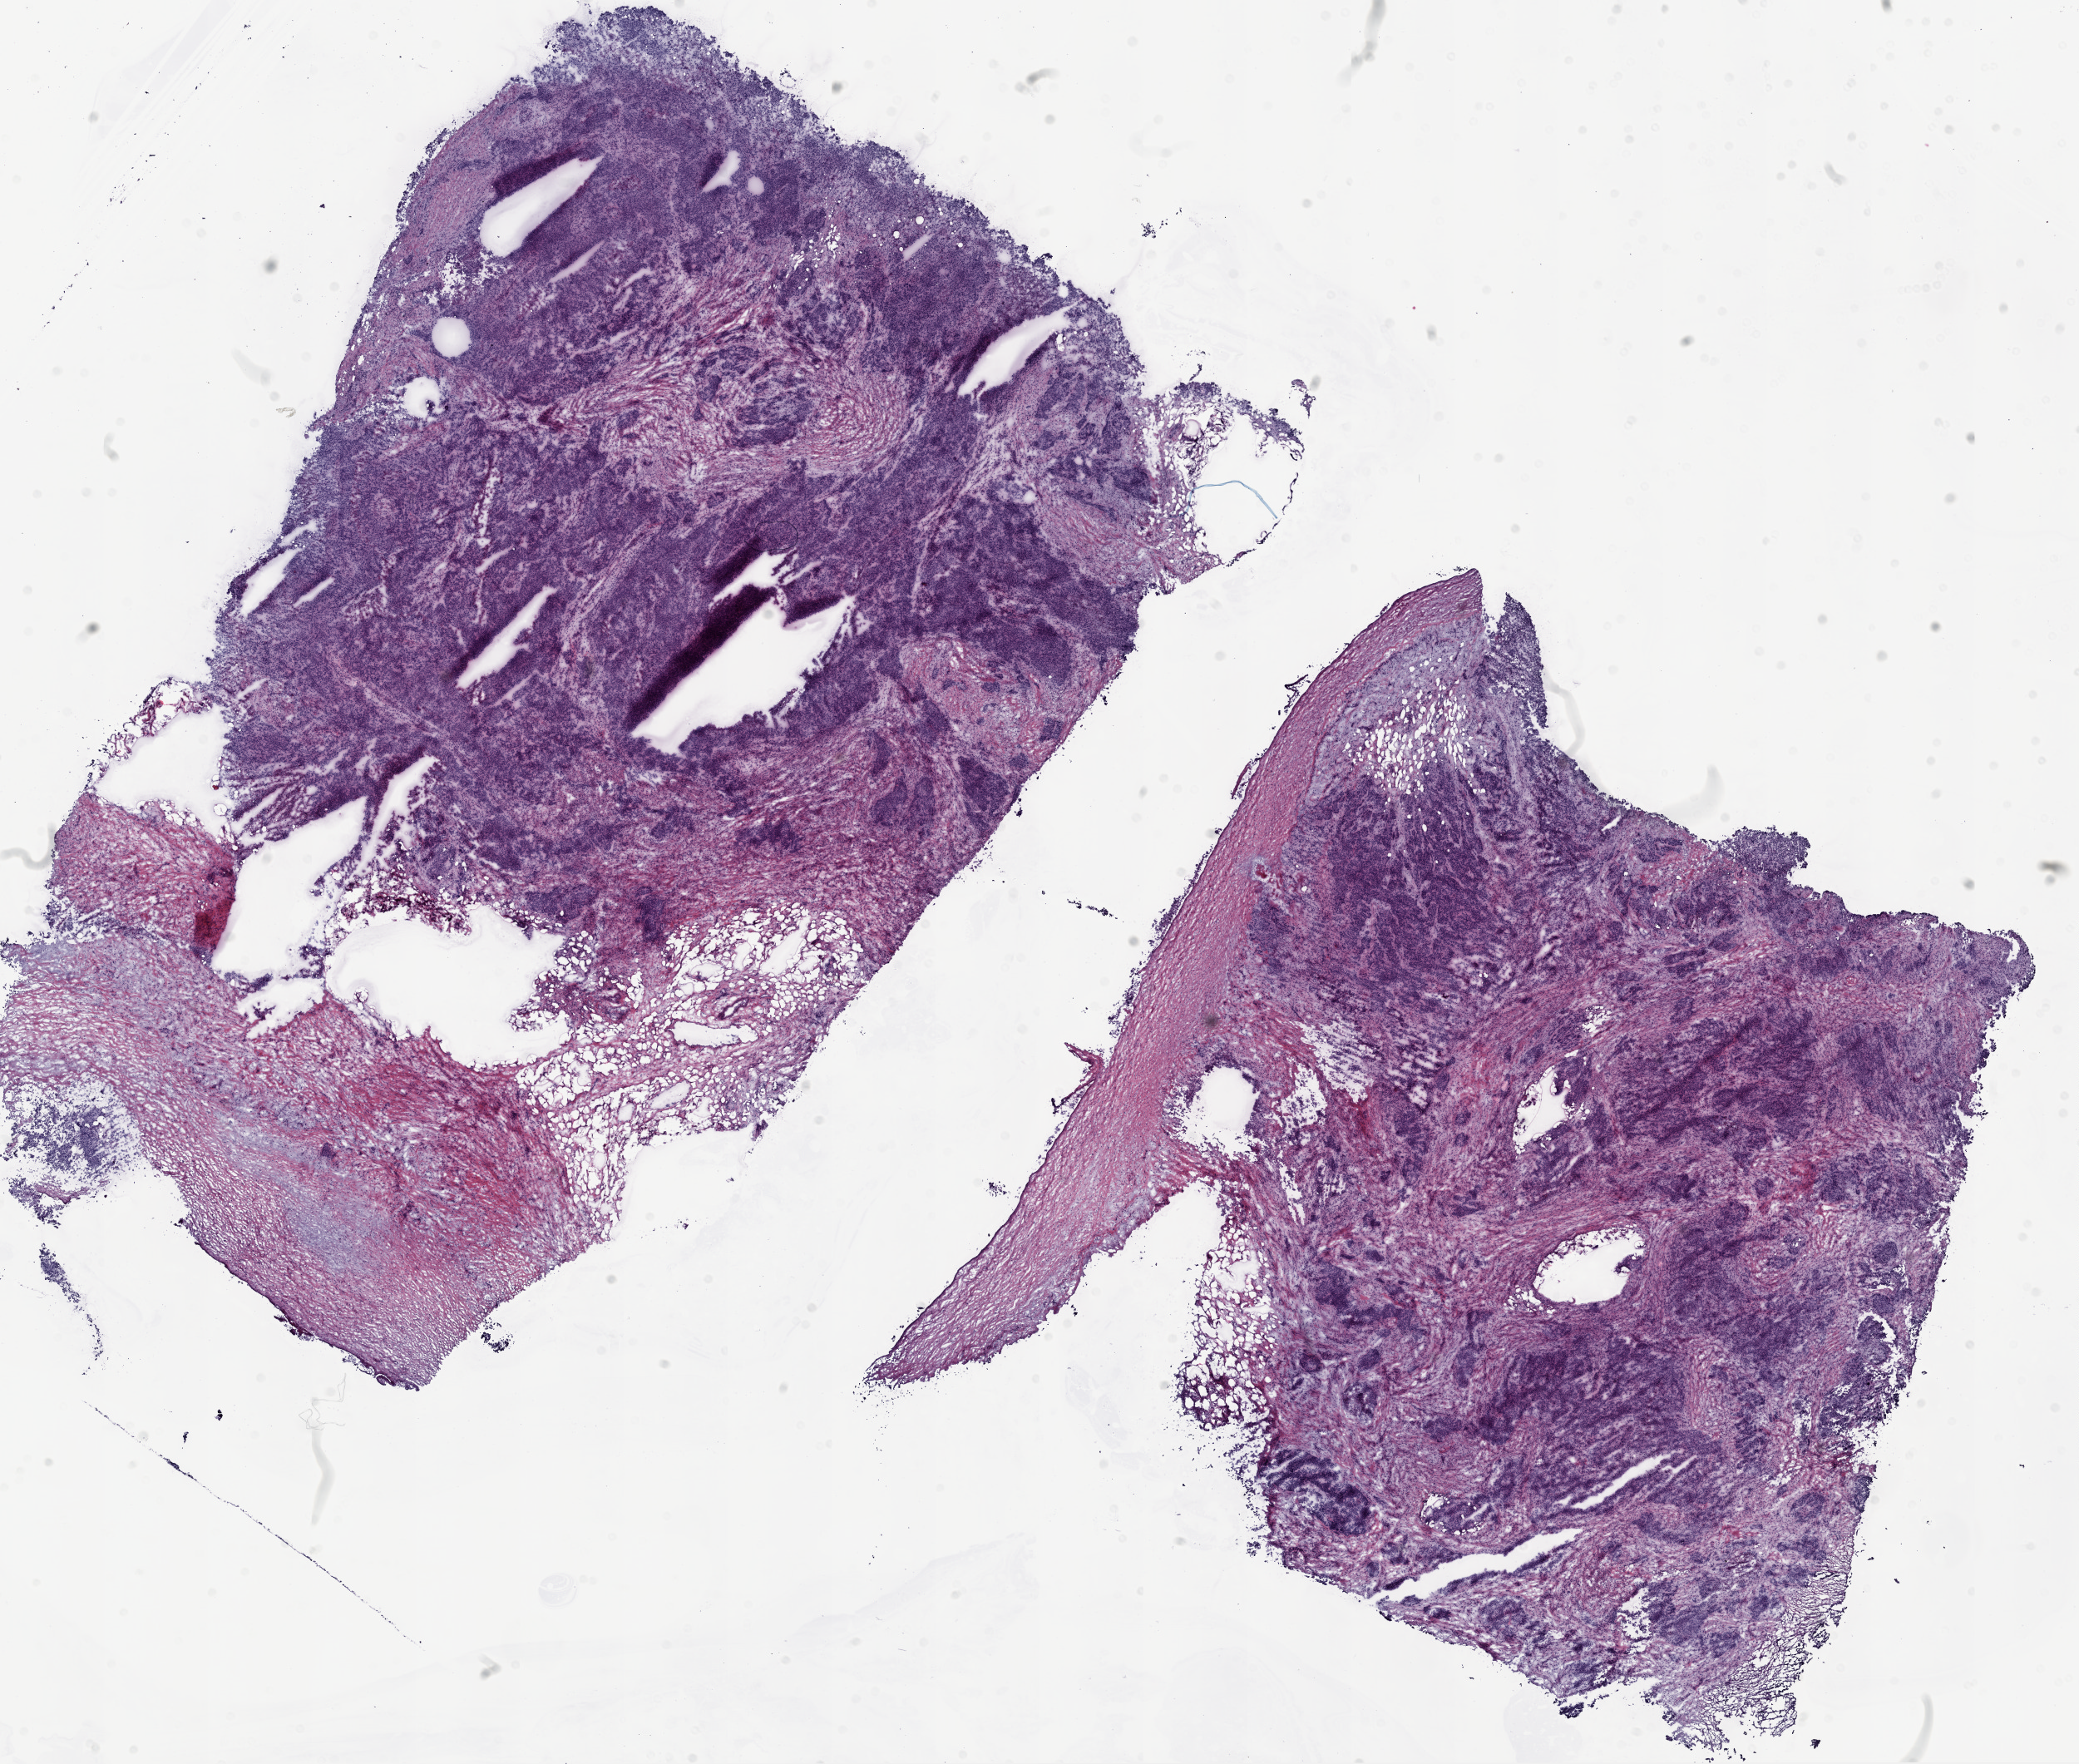
Digitized H&E-stained tissue section (whole slide), shown as a low-resolution overview of the whole scanned area (about 20.1 x 17.0 mm, from a 20x scan). Frozen section from the top of the tissue portion. Sample: primary tumour, ovary. Female patient; age at initial diagnosis 61 years. Histologic grade: G3 (poorly differentiated). Composition of this section per pathologist review: tumour cells 50%, tumour nuclei 70%, normal cells 0%, stromal cells 40%, necrosis 10%. Infiltration values recorded for this section: lymphocyte infiltration 40%, monocyte infiltration 10%, neutrophil infiltration 50%.
- FIGO stage: IIIC
- pathologic diagnosis: Serous cystadenocarcinoma, NOS